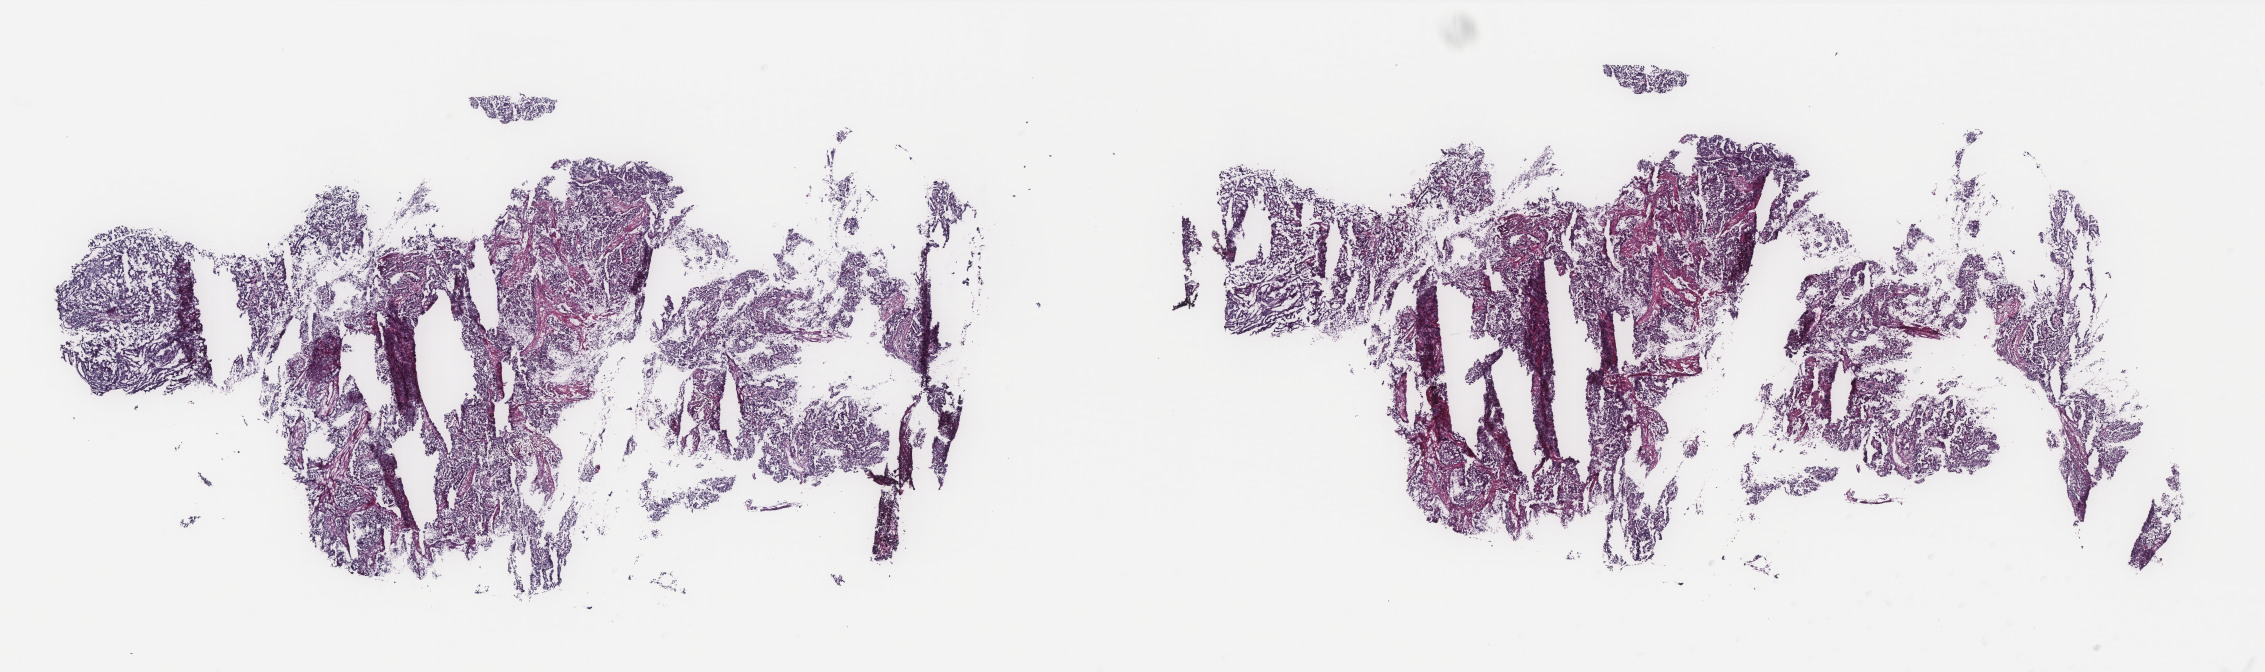
Whole-slide histology image, H&E — a low-resolution overview of the entire scanned area, about 36.3 x 10.8 mm, frozen section, uterus, primary tumour sample. Female, age 56 years at initial diagnosis. Histologic grade: G2 (moderately differentiated). Slide review estimates, as recorded: tumour cells 60%, tumour nuclei 70%, normal cells 30%, stromal cells 0%, necrosis 10%. Infiltration values recorded for this section: lymphocyte infiltration 1%, monocyte infiltration 0%, neutrophil infiltration 0%.
Pathologic diagnosis: Endometrioid adenocarcinoma, NOS (endometrium). FIGO stage: IIIA.